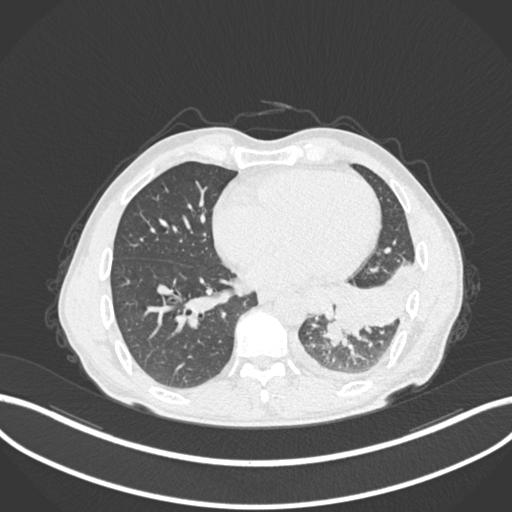
Chest CT, one axial slice. Slice 89 of 222 in the series (ordered by position). Reconstruction kernel B30f. 120 kVp. Lung window (W 1500 / L -600 HU). 1 mm slice thickness. 512 × 512 image matrix, field of view 400 × 400 mm. Male patient, age 47 years. From the clinical record (not read from this slice): clinical TNM (as recorded): T3 N1 M1c; histopathological grade: G3.
Structures marked on this image (rectangle marked by the reading radiologist):
- lung tumour (recorded histology: small cell carcinoma): box from (x=319, y=318) to (x=347, y=349) px